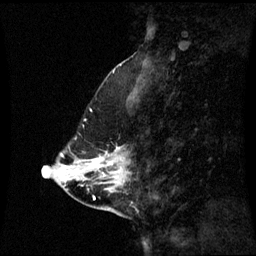
Breast MRI (dynamic contrast-enhanced), one sagittal slice. Position 21 of 60 along the scan axis. Dynamic contrast-enhanced series, image 2 of 3 at this slice position (ordered by acquisition). 1.5 T. TE 4.2 ms, TR 8.9 ms. 2.3 mm slice thickness. 256 × 256 image matrix, field of view 240 × 240 mm. Female patient, age 43 years. From the clinical record (not read from this slice): setting: breast cancer imaged before/during neoadjuvant chemotherapy; receptor status: HR-positive, HER2-negative.
Annotated regions visible in this slice (semi-automatically segmented with operator editing):
- analysis volume of interest (the breast-tissue region the enhancement analysis was run in; not a lesion): bounding box <78,148,128,193> (left, top, right, bottom; pixels)
- tumour enhancement mask (voxels above the 70 % enhancement threshold inside the analysis volume of interest): <96,164,105,177>